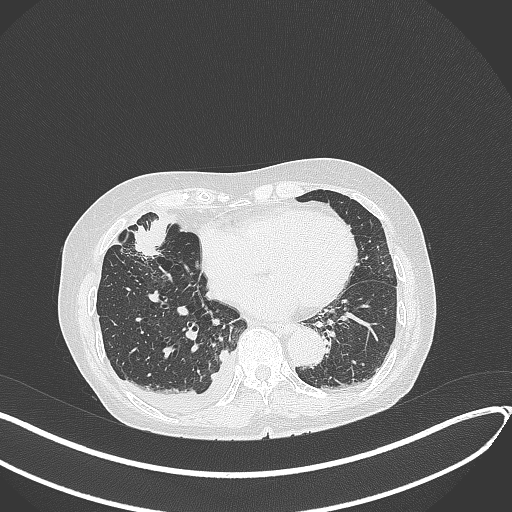
Chest CT, one axial slice; position 136 of 418 along the scan axis; lung window (W 1500 / L -600 HU); 1 mm slice thickness; 512 × 512 image matrix, field of view 400 × 400 mm. Patient: female, 75 years. From the clinical record (not read from this slice): clinical TNM (as recorded): T2a N3 M0.
Outlined on this slice (bounding box drawn by a radiologist):
- lung tumour (recorded histology: adenocarcinoma): bounding box <128,226,166,259> (left, top, right, bottom; pixels)